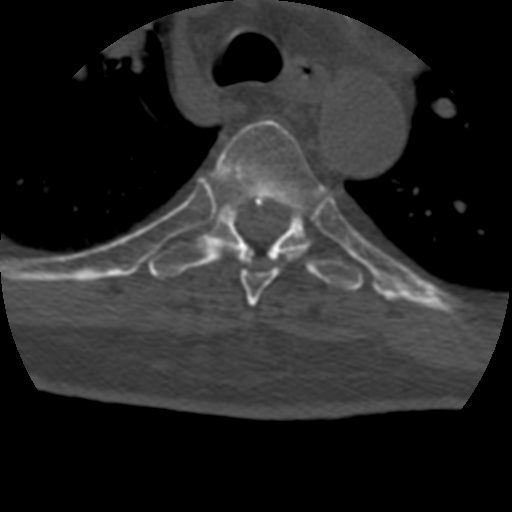
CT including the spine, one axial slice. Slice 311 of 399 in the series (ordered by position). Reconstruction kernel STANDARD. 120 kVp. Bone window (W 1800 / L 400 HU). 1.25 mm slice thickness. 512 × 512 image matrix. Patient age 69 years. From the clinical record (not read from this slice): primary cancer: prostate.
Outlined on this slice (semi-automatically segmented with operator editing):
- T5 vertebra: bounding box <205,120,325,307> (left, top, right, bottom; pixels)
- T6 vertebra: <148,200,364,291>